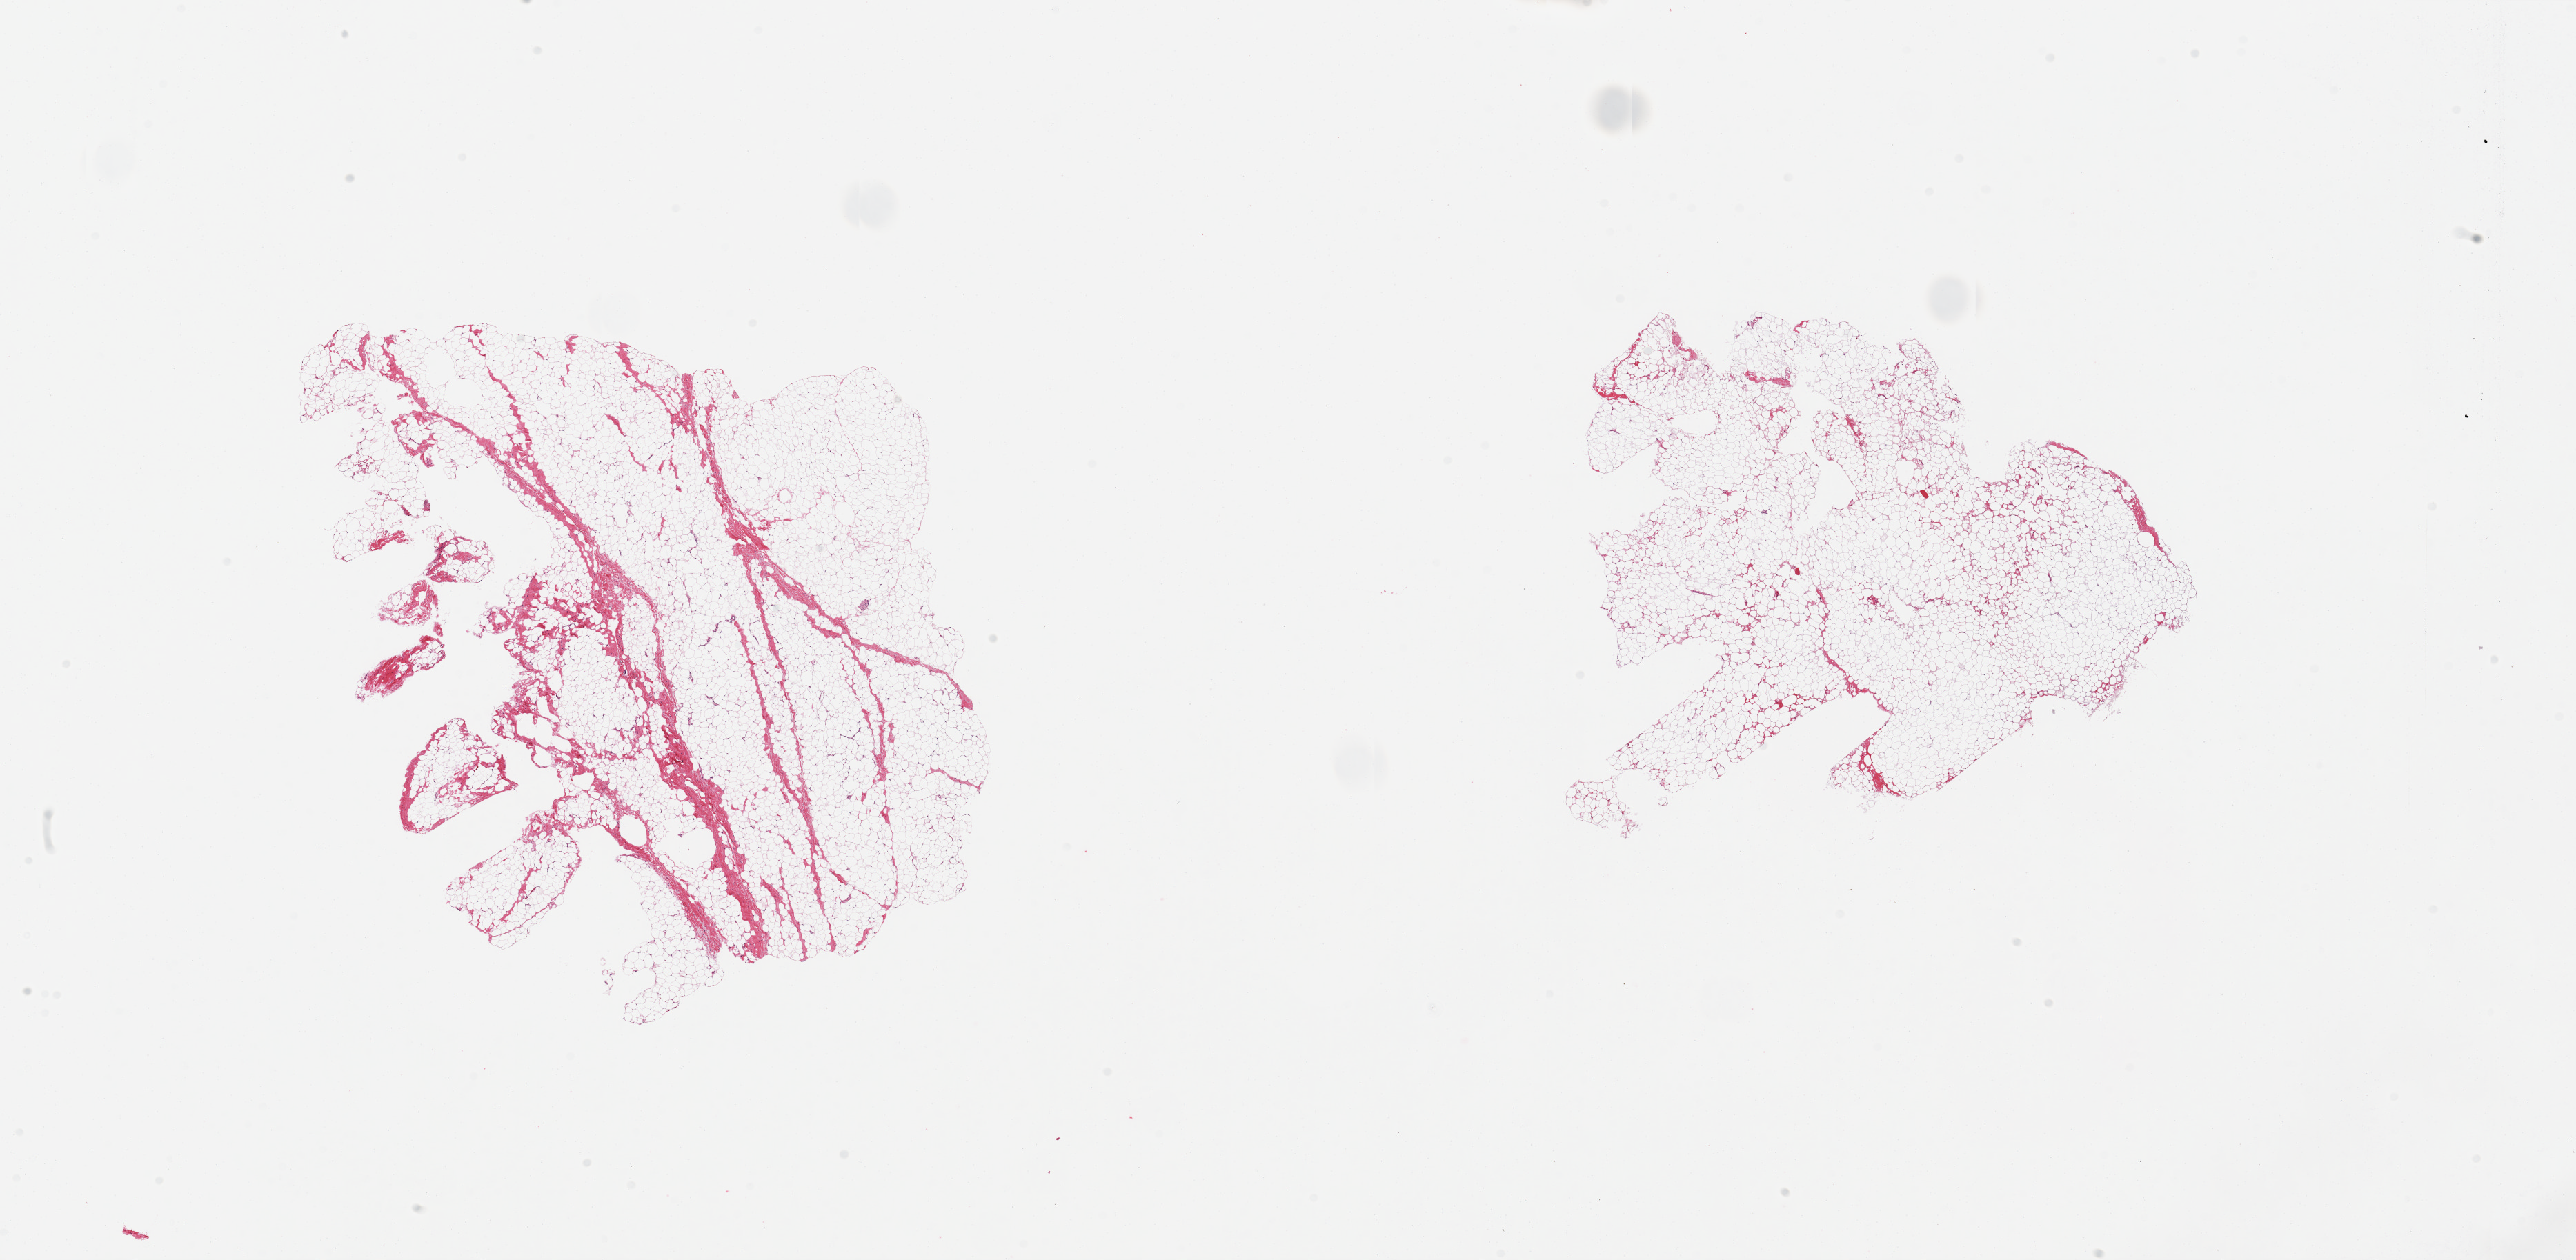
Hematoxylin and eosin (H&E) whole-slide image, shown as a low-resolution overview of the whole scanned area (about 29.5 x 14.5 mm, acquisition: 20x scan), PAXgene-fixed, paraffin-embedded tissue, target tissue: breast, donor tissue sample.
Reviewer comment on this tissue sample: 2 pieces; 5% fibrous content in 1; no ducts.